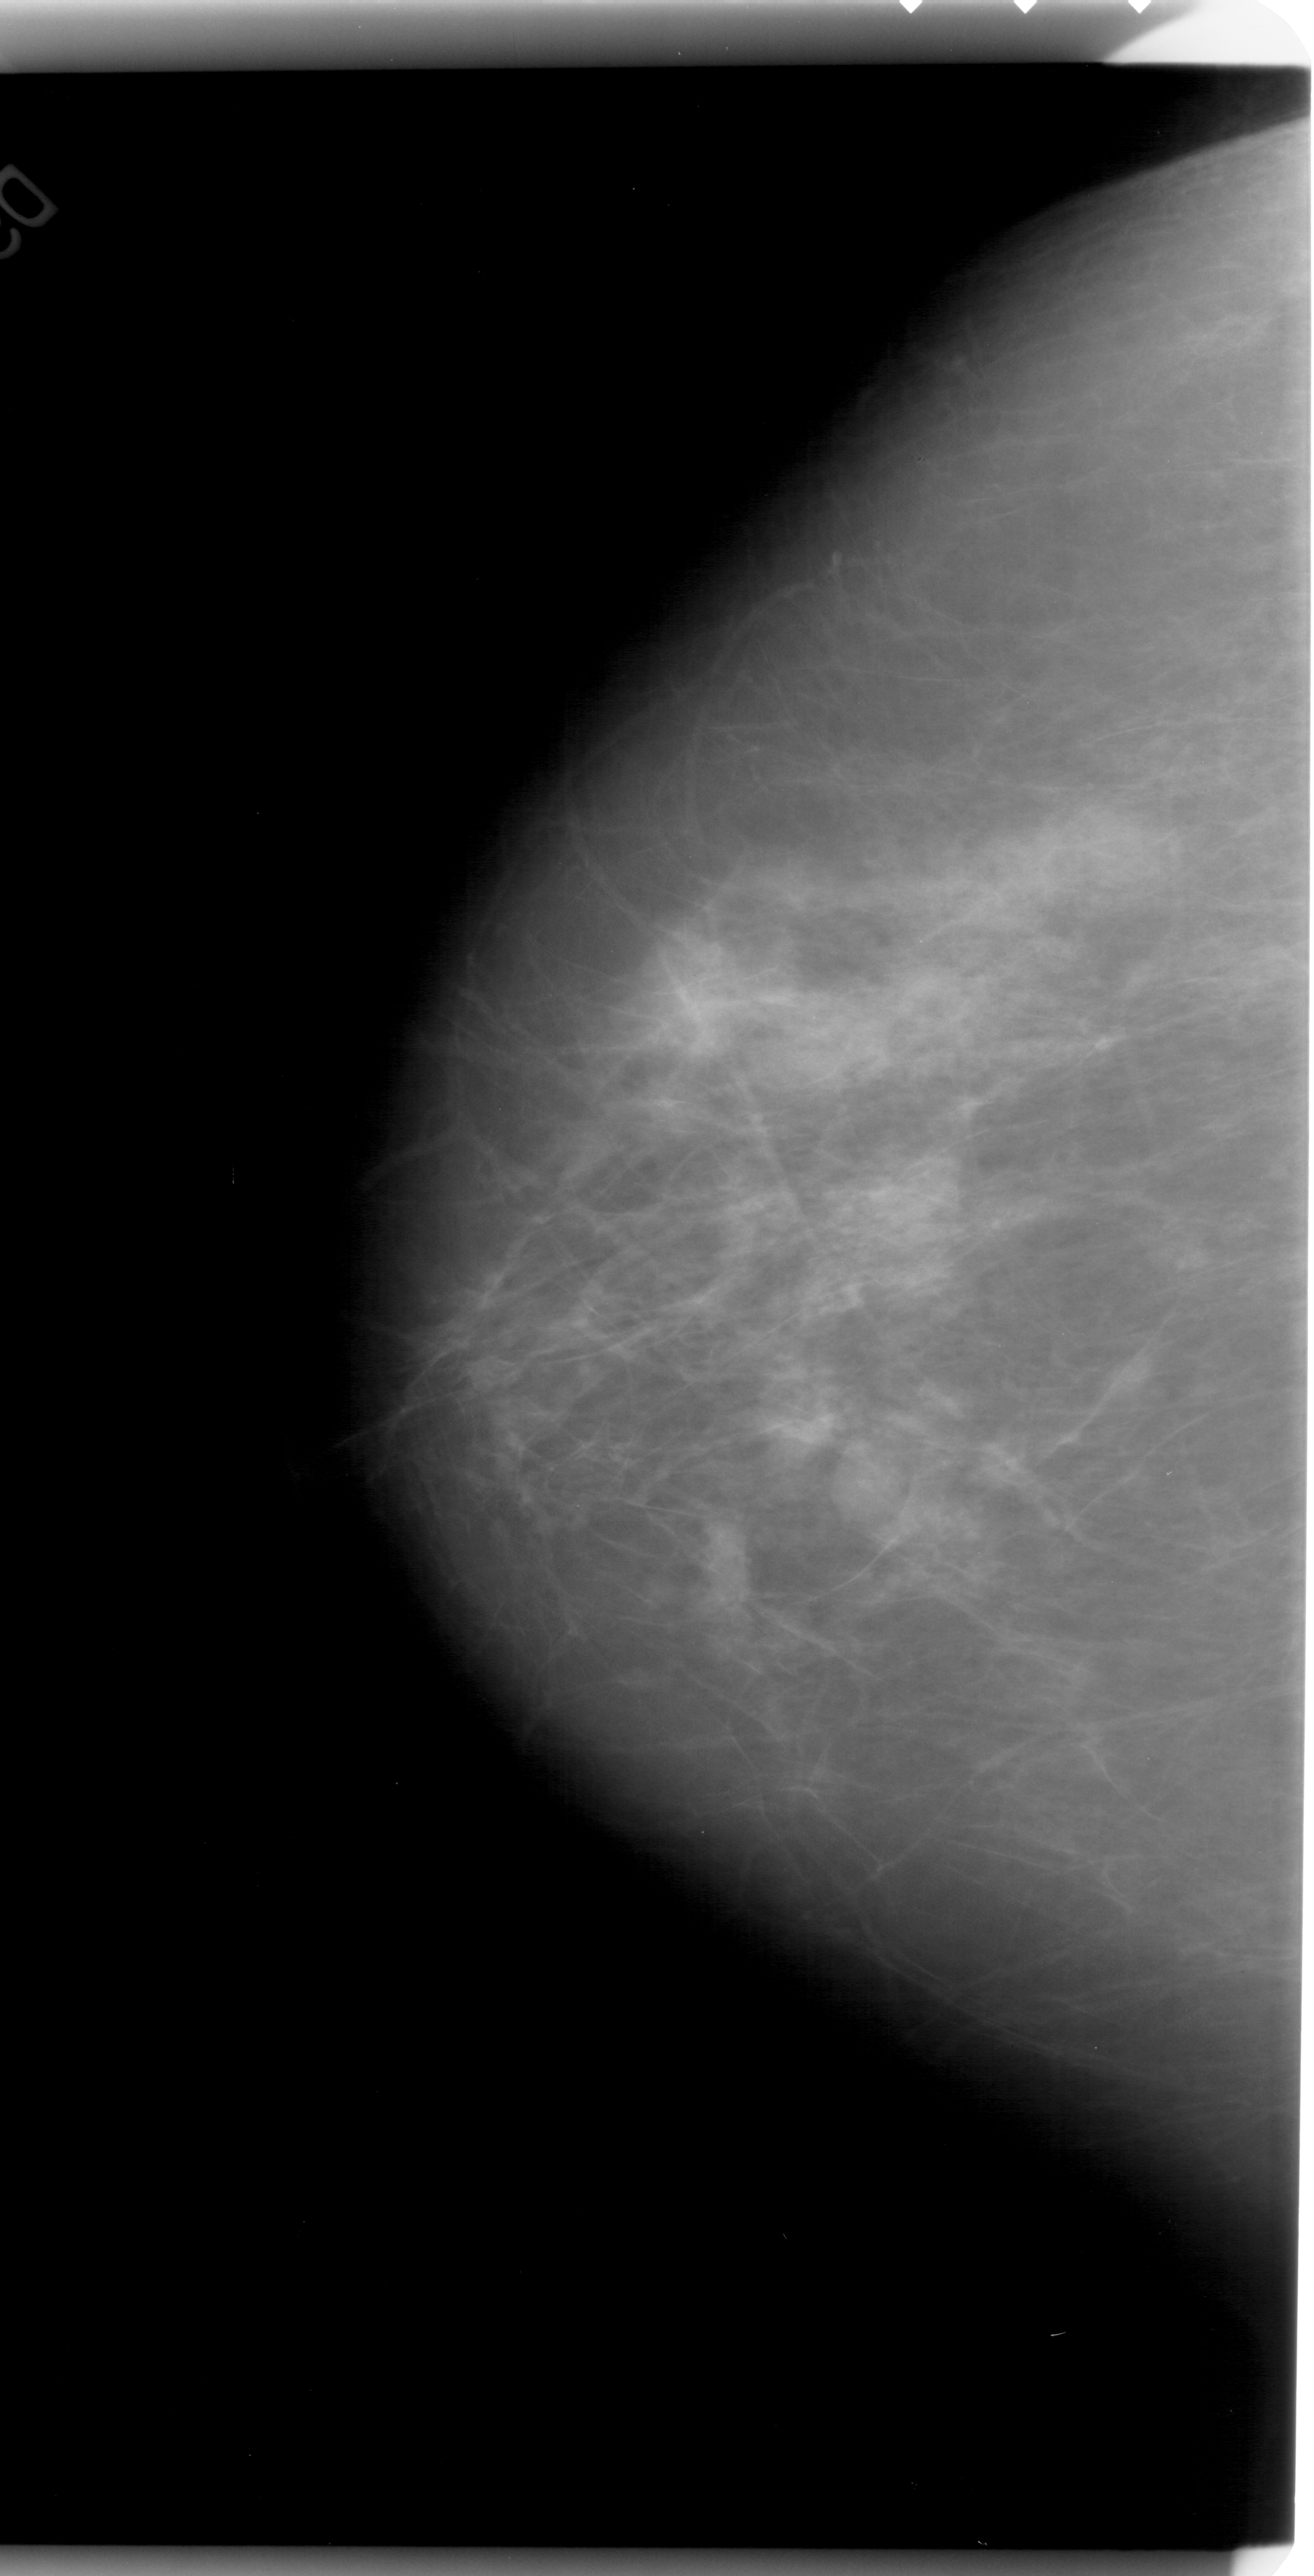
Digitized screen-film mammogram, left breast, CC view, BI-RADS breast density category 2 (scale 1–4).
- Radiologist-marked abnormalities on this image: mass, shape oval, margins obscured; BI-RADS assessment category 3; subtlety rating 3 on a 1 (subtle) to 5 (obvious) scale; pathology result (as recorded, not read from the image): benign.